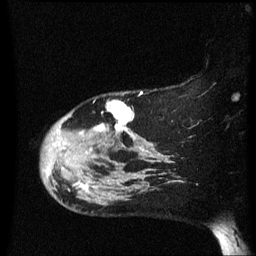
Breast MRI (dynamic contrast-enhanced), one sagittal slice. Position 50 of 60 along the scan axis. Dynamic contrast-enhanced series, image 2 of 3 at this slice position (ordered by acquisition). 1.5 T. TE 4.2 ms, TR 8.4 ms. 2.2 mm slice thickness. 256 × 256 image matrix, field of view 200 × 200 mm. Patient: female, 47 years.
Structures marked on this image (semi-automatic segmentation, software-assisted and operator-edited):
- analysis volume of interest (the breast-tissue region the enhancement analysis was run in; not a lesion): bounding box [x1, y1, x2, y2] px = [42, 101, 149, 206]
- tumour enhancement mask (voxels above the 70 % enhancement threshold inside the analysis volume of interest): [78, 101, 145, 193]